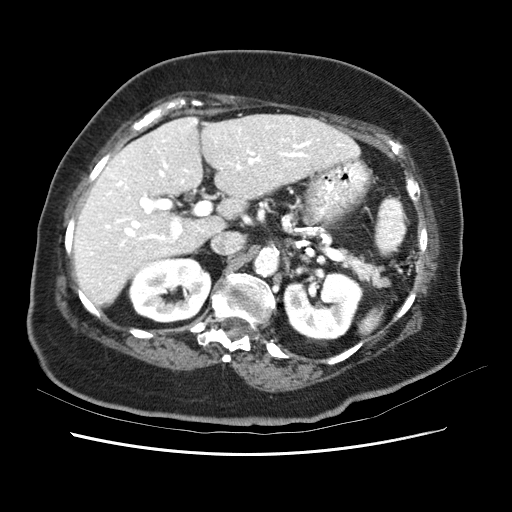
Contrast-enhanced abdominal CT (liver protocol), one axial slice. Position 33 of 62 along the scan axis. 120 kVp. Soft-tissue window (W 400 / L 40 HU). 2.5 mm slice thickness. 512 × 512 image matrix, field of view 340 × 340 mm. From the clinical record (not read from this slice): diagnosis: hepatocellular carcinoma (patient treated with transarterial chemoembolisation; whether this scan precedes or follows treatment is not stated here); TNM stage (as recorded): Stage-I; Child-Pugh class: B; tumour nodularity: uninodular; tumour size: 5.3 cm.
Outlined on this slice (semi-automatically segmented with operator editing):
- liver parenchyma outside the tumour (the mass and vessels are separate outlines, so this box may not span the whole liver): bounding box <76,113,360,306> (left, top, right, bottom; pixels)
- liver vessels: <80,118,351,286>